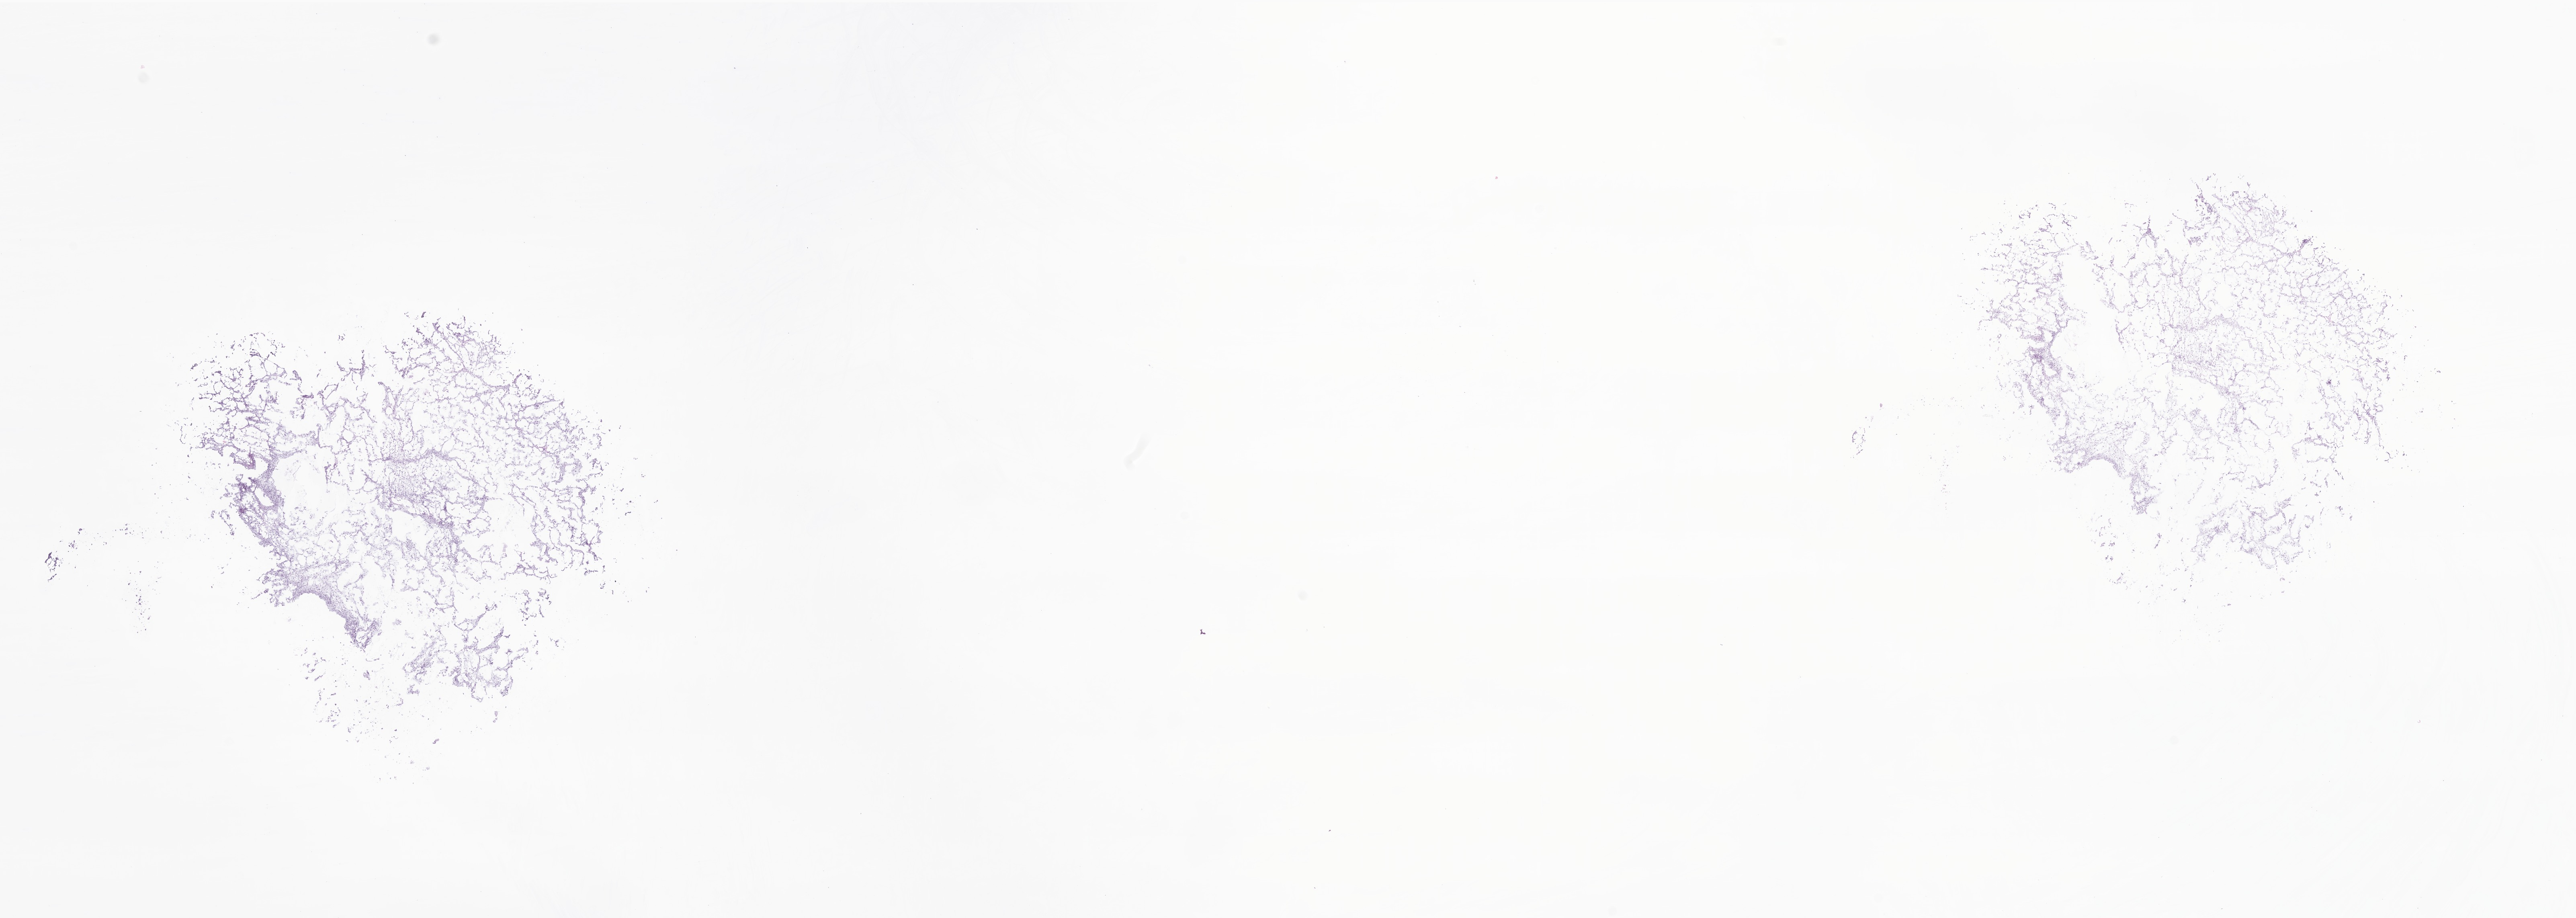
Whole-slide image, haematoxylin and eosin stain of tumor tissue from the brain — whole scanned area (about 27.0 x 9.6 mm) shown as a low-resolution overview. Frozen section (OCT-embedded). Male patient, age 133 months (11 years 1 month).
Recorded diagnosis: Atypical teratoid/rhabdoid tumor.